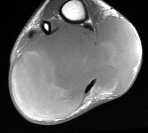
MRI of an extremity soft-tissue mass, one axial slice; position 27 of 76 along the scan axis; MR volume resampled by the dataset authors to the PET/CT grid (not the native acquisition matrix); 3.27 mm slice thickness; 148 × 133 image matrix, field of view 145 × 130 mm. Male patient. Case-level facts recorded for this patient, not image findings: histological type: liposarcoma - round cell; grade: high; site of the primary tumour: right calf.
Structures marked on this image (expert contour drawn on MRI and transferred to this co-registered scan by the dataset authors):
- gross tumour volume (mass): bounding box [x1, y1, x2, y2] px = [13, 16, 141, 116]